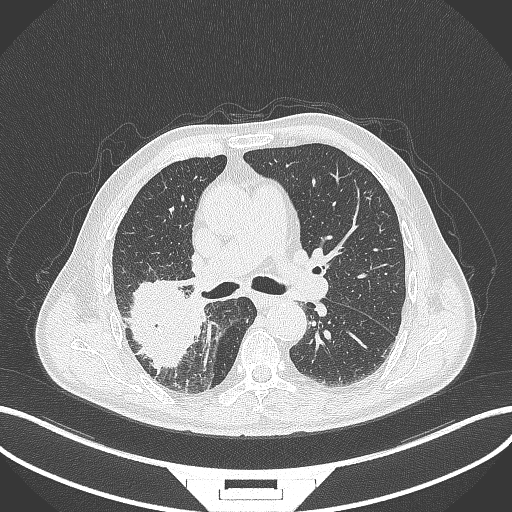
Chest CT, one axial slice. Position 246 of 429 along the scan axis. Reconstruction kernel B70f. 120 kVp. Lung window (W 1500 / L -600 HU). 1 mm slice thickness. 512 × 512 image matrix, field of view 400 × 400 mm. Patient: male, 72 years. Case-level facts recorded for this patient, not image findings: clinical TNM (as recorded): T3 N2 M0.
Annotated regions visible in this slice (bounding box drawn by a radiologist):
- lung tumour (recorded histology: adenocarcinoma): bounding box (x1, y1, x2, y2) in pixels: (121, 275, 206, 373)